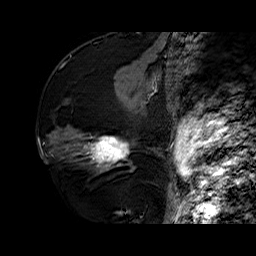
Breast MRI (dynamic contrast-enhanced), one sagittal slice. Position 29 of 60 along the scan axis. Dynamic contrast-enhanced series, time point 2 of 6 at this slice position (early post-contrast). 1.5 T. TE 6.4 ms, TR 32.7 ms. 256 × 256 image matrix. Female patient. From the clinical record (not read from this slice): setting: breast cancer imaged before/during neoadjuvant chemotherapy; receptor status: HR-positive, HER2-negative.
Structures marked on this image (semi-automatic segmentation, software-assisted and operator-edited):
- analysis volume of interest (the breast-tissue region the enhancement analysis was run in; not a lesion): box from (x=73, y=110) to (x=141, y=174) px
- tumour enhancement mask (voxels above the 100 % enhancement threshold inside the analysis volume of interest): (x=85, y=136)–(x=130, y=165)